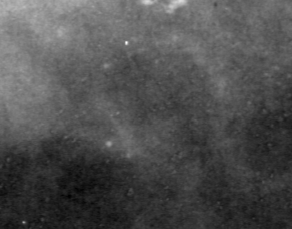
Region of interest cut from a scanned film mammogram (one marked finding); left breast; CC view; BI-RADS breast density category 4 (scale 1–4).
Finding: calcifications, morphology pleomorphic, distribution clustered; BI-RADS assessment category 4; pathology result (as recorded, not read from the image): malignant.